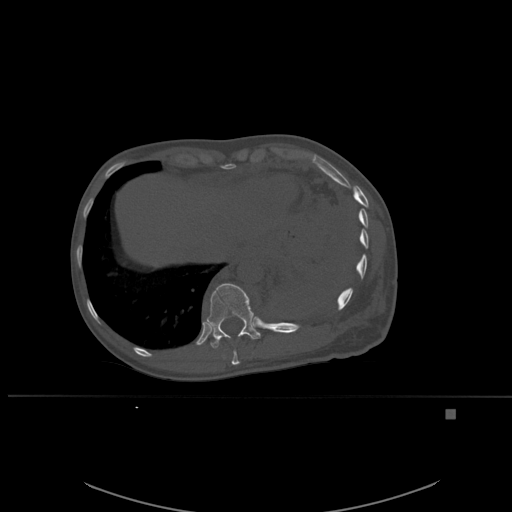
CT including the spine, one axial slice. Position 304 of 537 along the scan axis. Bone window (W 1800 / L 400 HU). 1.5 mm slice thickness. 512 × 512 image matrix. Patient: female, 45 years. From the clinical record (not read from this slice): primary cancer: lung.
Structures marked on this image (semi-automatically segmented with operator editing):
- T10 vertebra: bounding box [x1, y1, x2, y2] px = [231, 349, 240, 365]
- T11 vertebra: [206, 283, 261, 349]